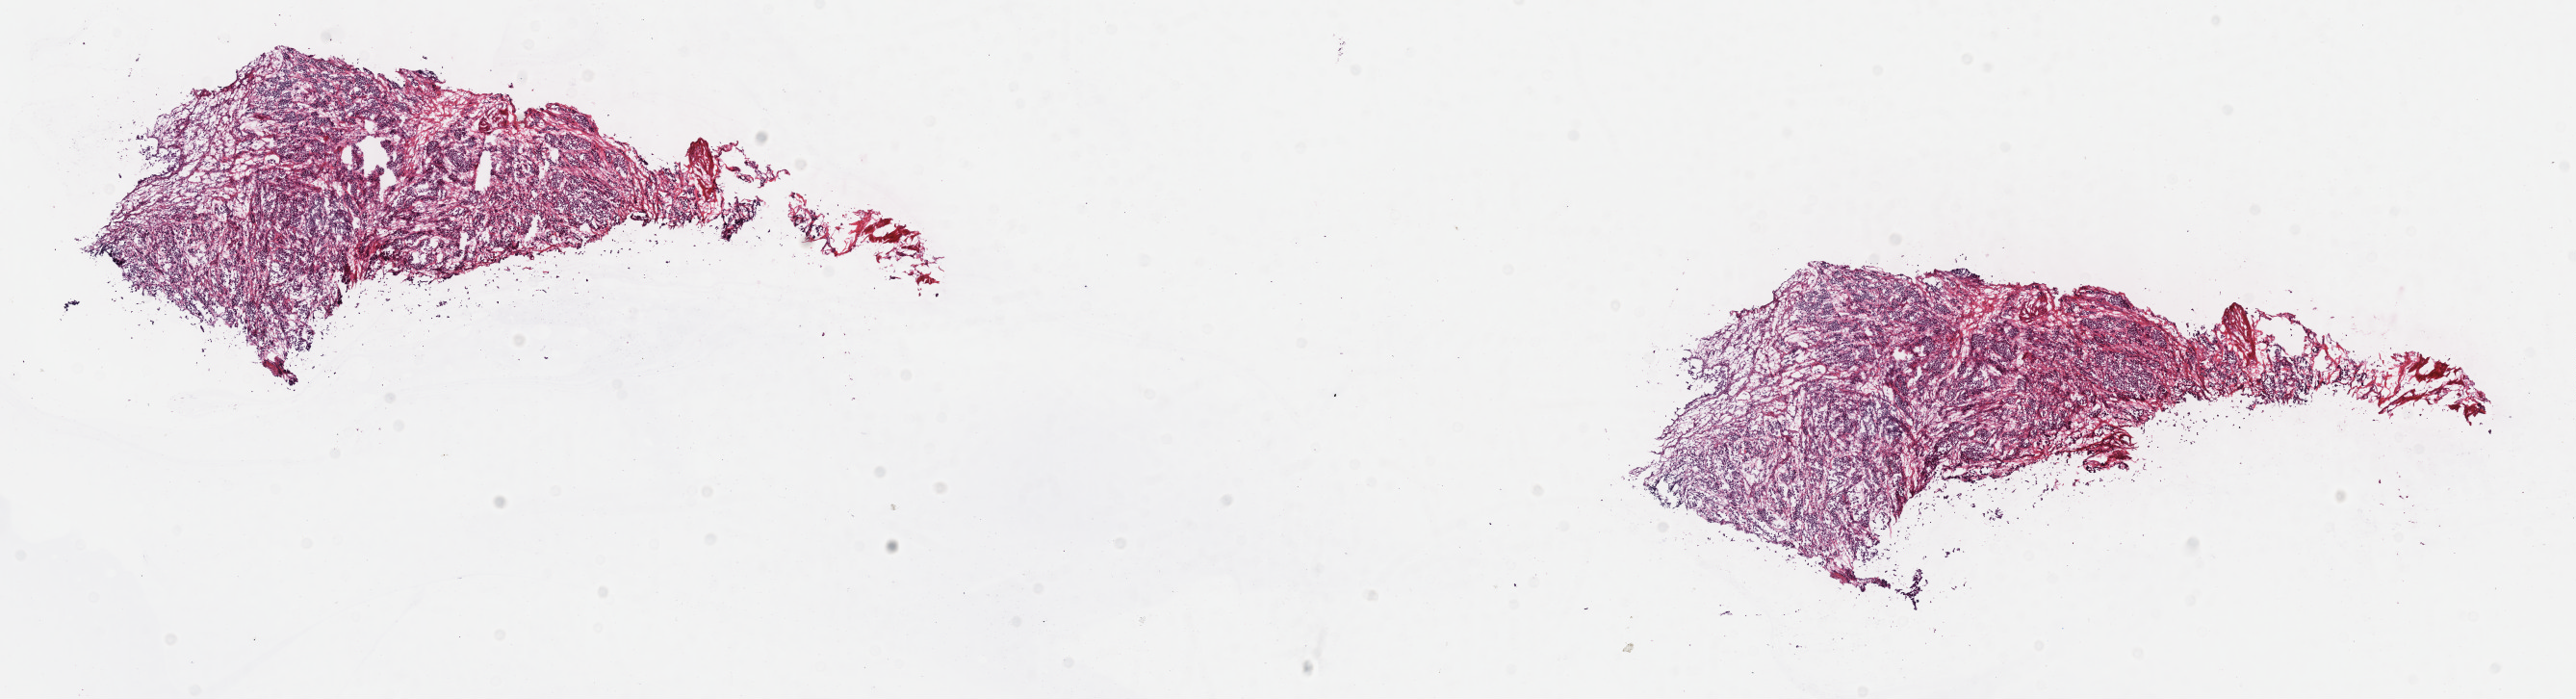
Whole-slide histology image, H&E-stained, low-resolution overview of the scanned area, about 21.6 x 5.9 mm (from a 40x scan). Frozen section from the top of the tissue portion. Primary tumour sample from the bladder. Male patient; age at initial diagnosis 66 years. Histologic grade: high grade. Composition of this section per pathologist review: tumour cells 60%, tumour nuclei 70%, normal cells 0%, stromal cells 40%, necrosis 0%. Inflammatory infiltration, as recorded: lymphocyte infiltration 0%, monocyte infiltration 0%, neutrophil infiltration 0%.
Histologic diagnosis: Transitional cell carcinoma (anterior wall of bladder). Lymph nodes positive (case pathology): 3 of 14 examined. AJCC pathologic stage: IV. TNM: T4a N1 M0.